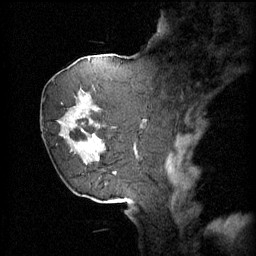
Breast MRI (dynamic contrast-enhanced), one sagittal slice. 4 images stored at this slice position (order not interpretable as contrast timing). 1.5 T. TE 4.2 ms, TR 11 ms. 256 × 256 image matrix. Female patient, age 72 years.
Annotated regions visible in this slice (semi-automatic segmentation, software-assisted and operator-edited):
- analysis volume of interest (the breast-tissue region the enhancement analysis was run in; not a lesion): box from (x=49, y=68) to (x=109, y=163) px
- tumour enhancement mask (voxels above the 70 % enhancement threshold inside the analysis volume of interest): (x=64, y=88)–(x=109, y=159)